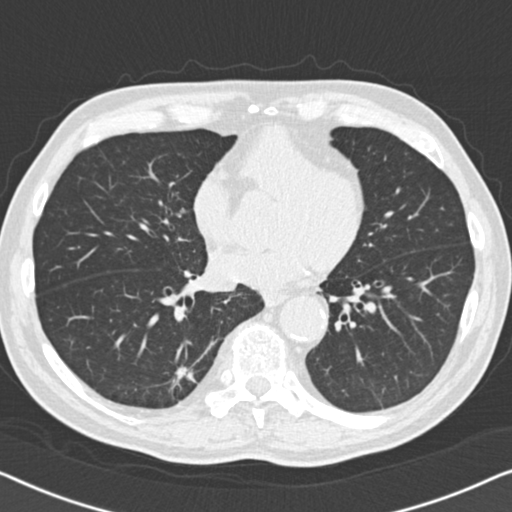
Low-dose screening chest CT, one axial slice; slice 59 of 164 in the series (ordered by position); reconstruction kernel B30f; 120 kVp; lung window (W 1500 / L -600 HU); 512 × 512 image matrix, field of view 330 × 330 mm.
Outlined on this slice (expert manual segmentation):
- lesion 1 (tumor, lower lobe of right lung): bounding box [x1, y1, x2, y2] px = [172, 366, 195, 385]